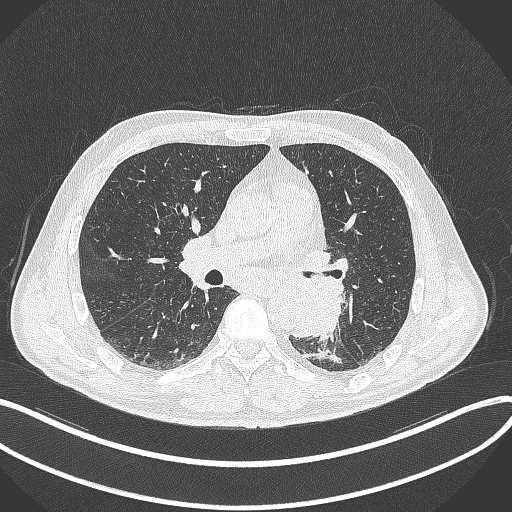
Chest CT, one axial slice. Slice 183 of 329 in the series (ordered by position). 120 kVp. Lung window (W 1500 / L -600 HU). 512 × 512 image matrix, field of view 400 × 400 mm. Male patient, age 59 years. Case-level facts recorded for this patient, not image findings: clinical TNM (as recorded): T2a N2 M0.
Annotated regions visible in this slice (rectangle marked by the reading radiologist):
- lung tumour (recorded histology: squamous cell carcinoma): bounding box (x1, y1, x2, y2) in pixels: (284, 270, 349, 342)